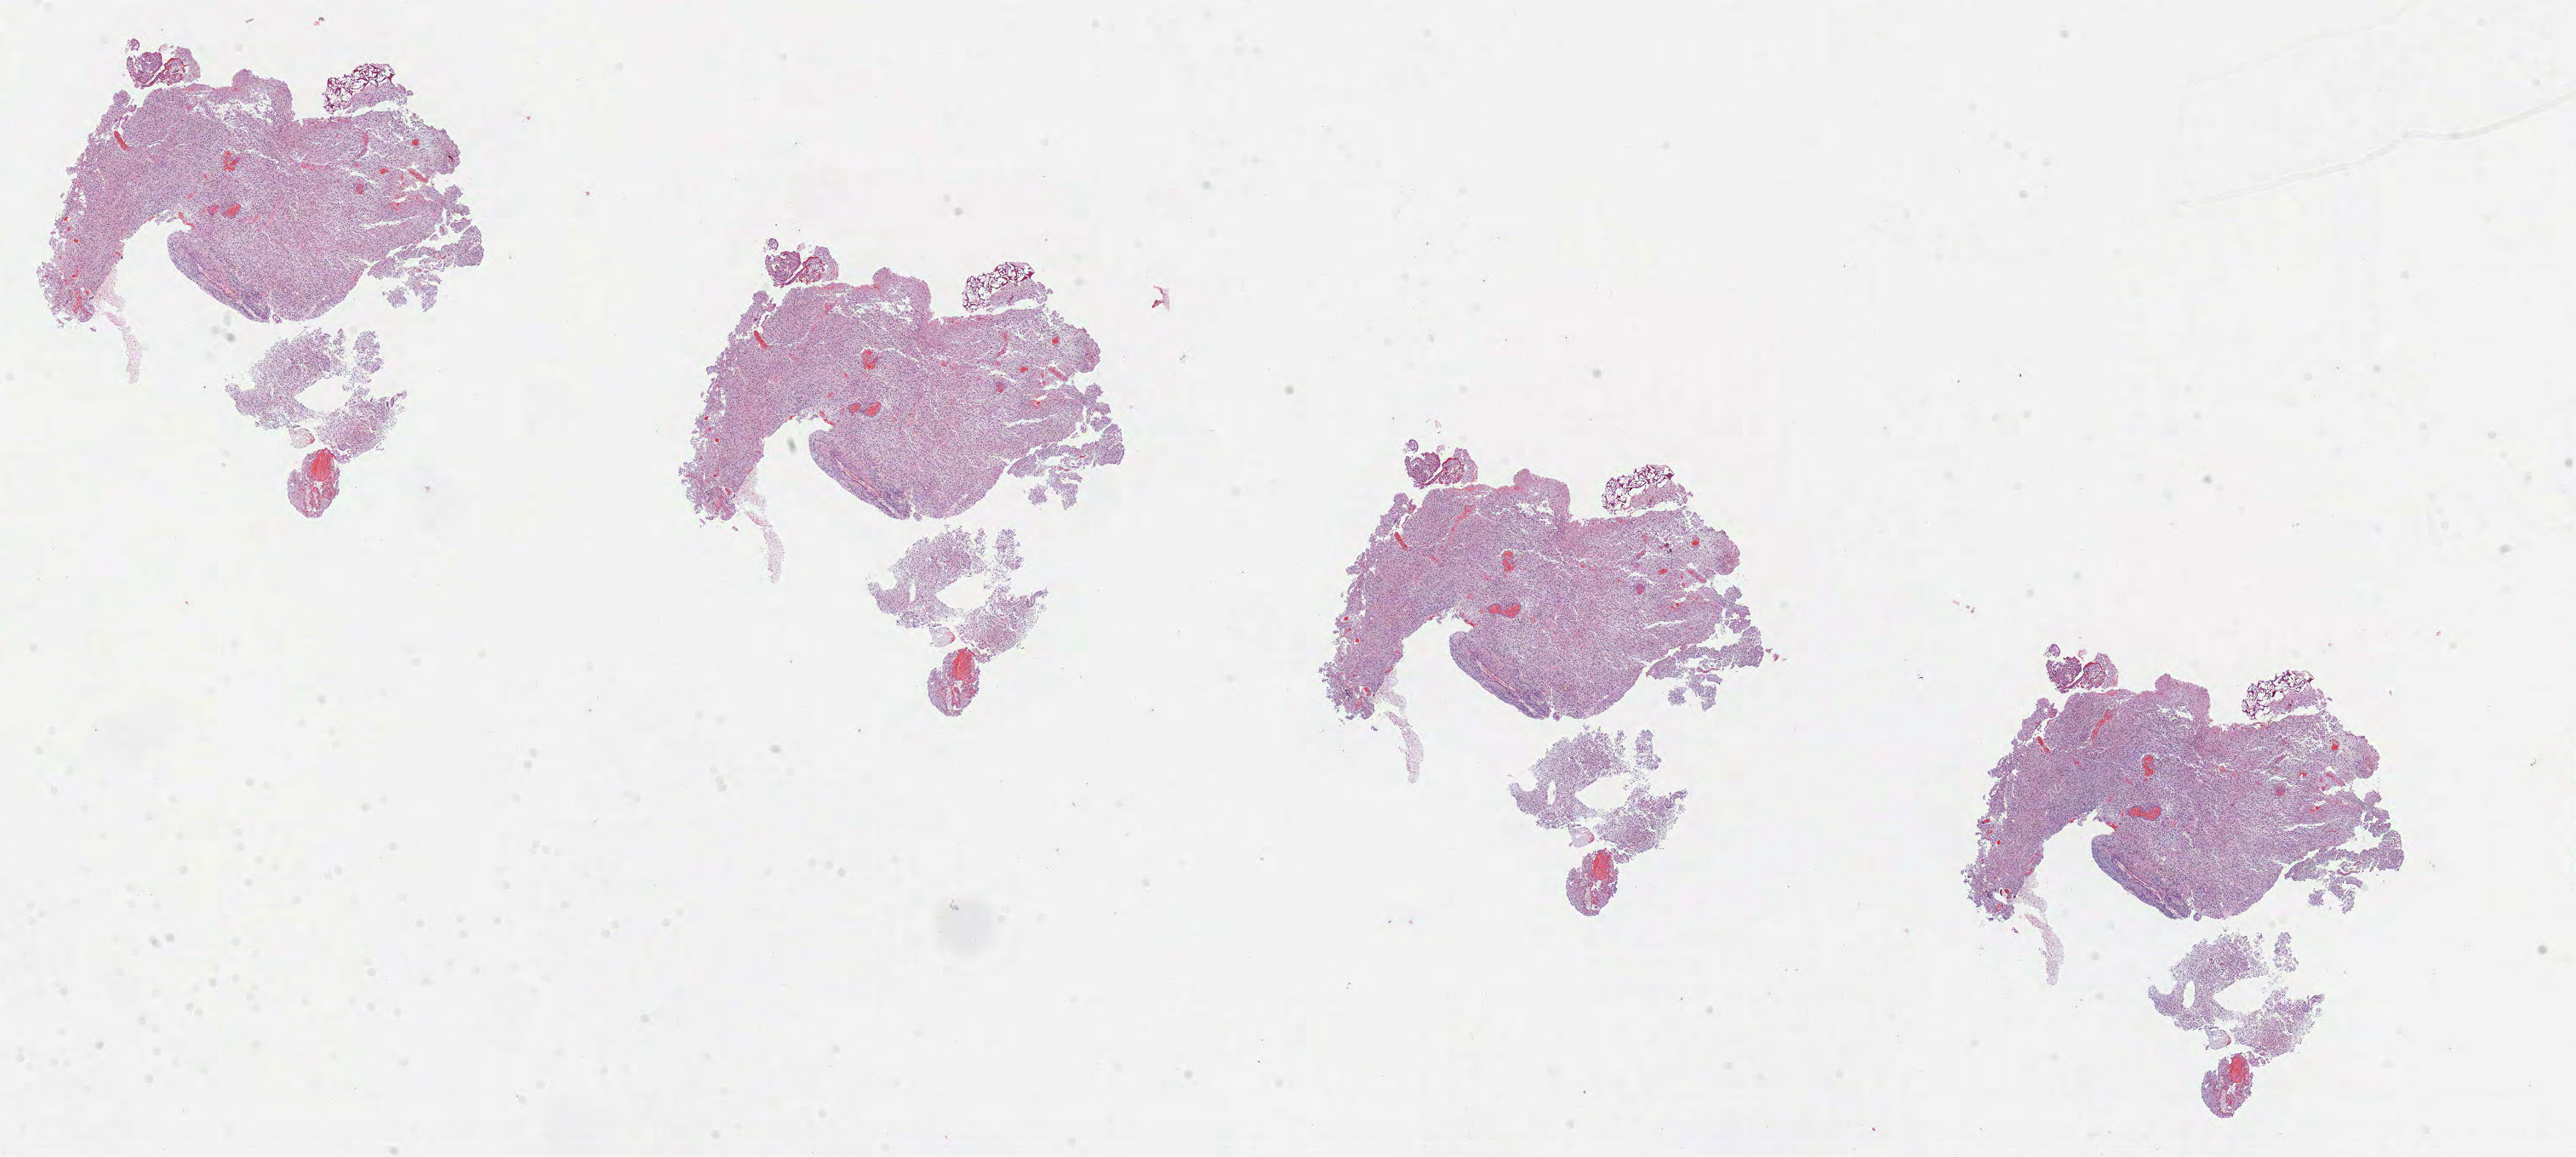
Digitized Hematoxylin and eosin (H&E) stained tissue section (whole slide) — shown as a low-resolution overview of the whole scanned area (about 24.4 x 11.0 mm, from a 40x scan); FFPE section; brain, primary tumour sample. Male patient; age at initial diagnosis 61 years.
• histologic diagnosis: Glioblastoma